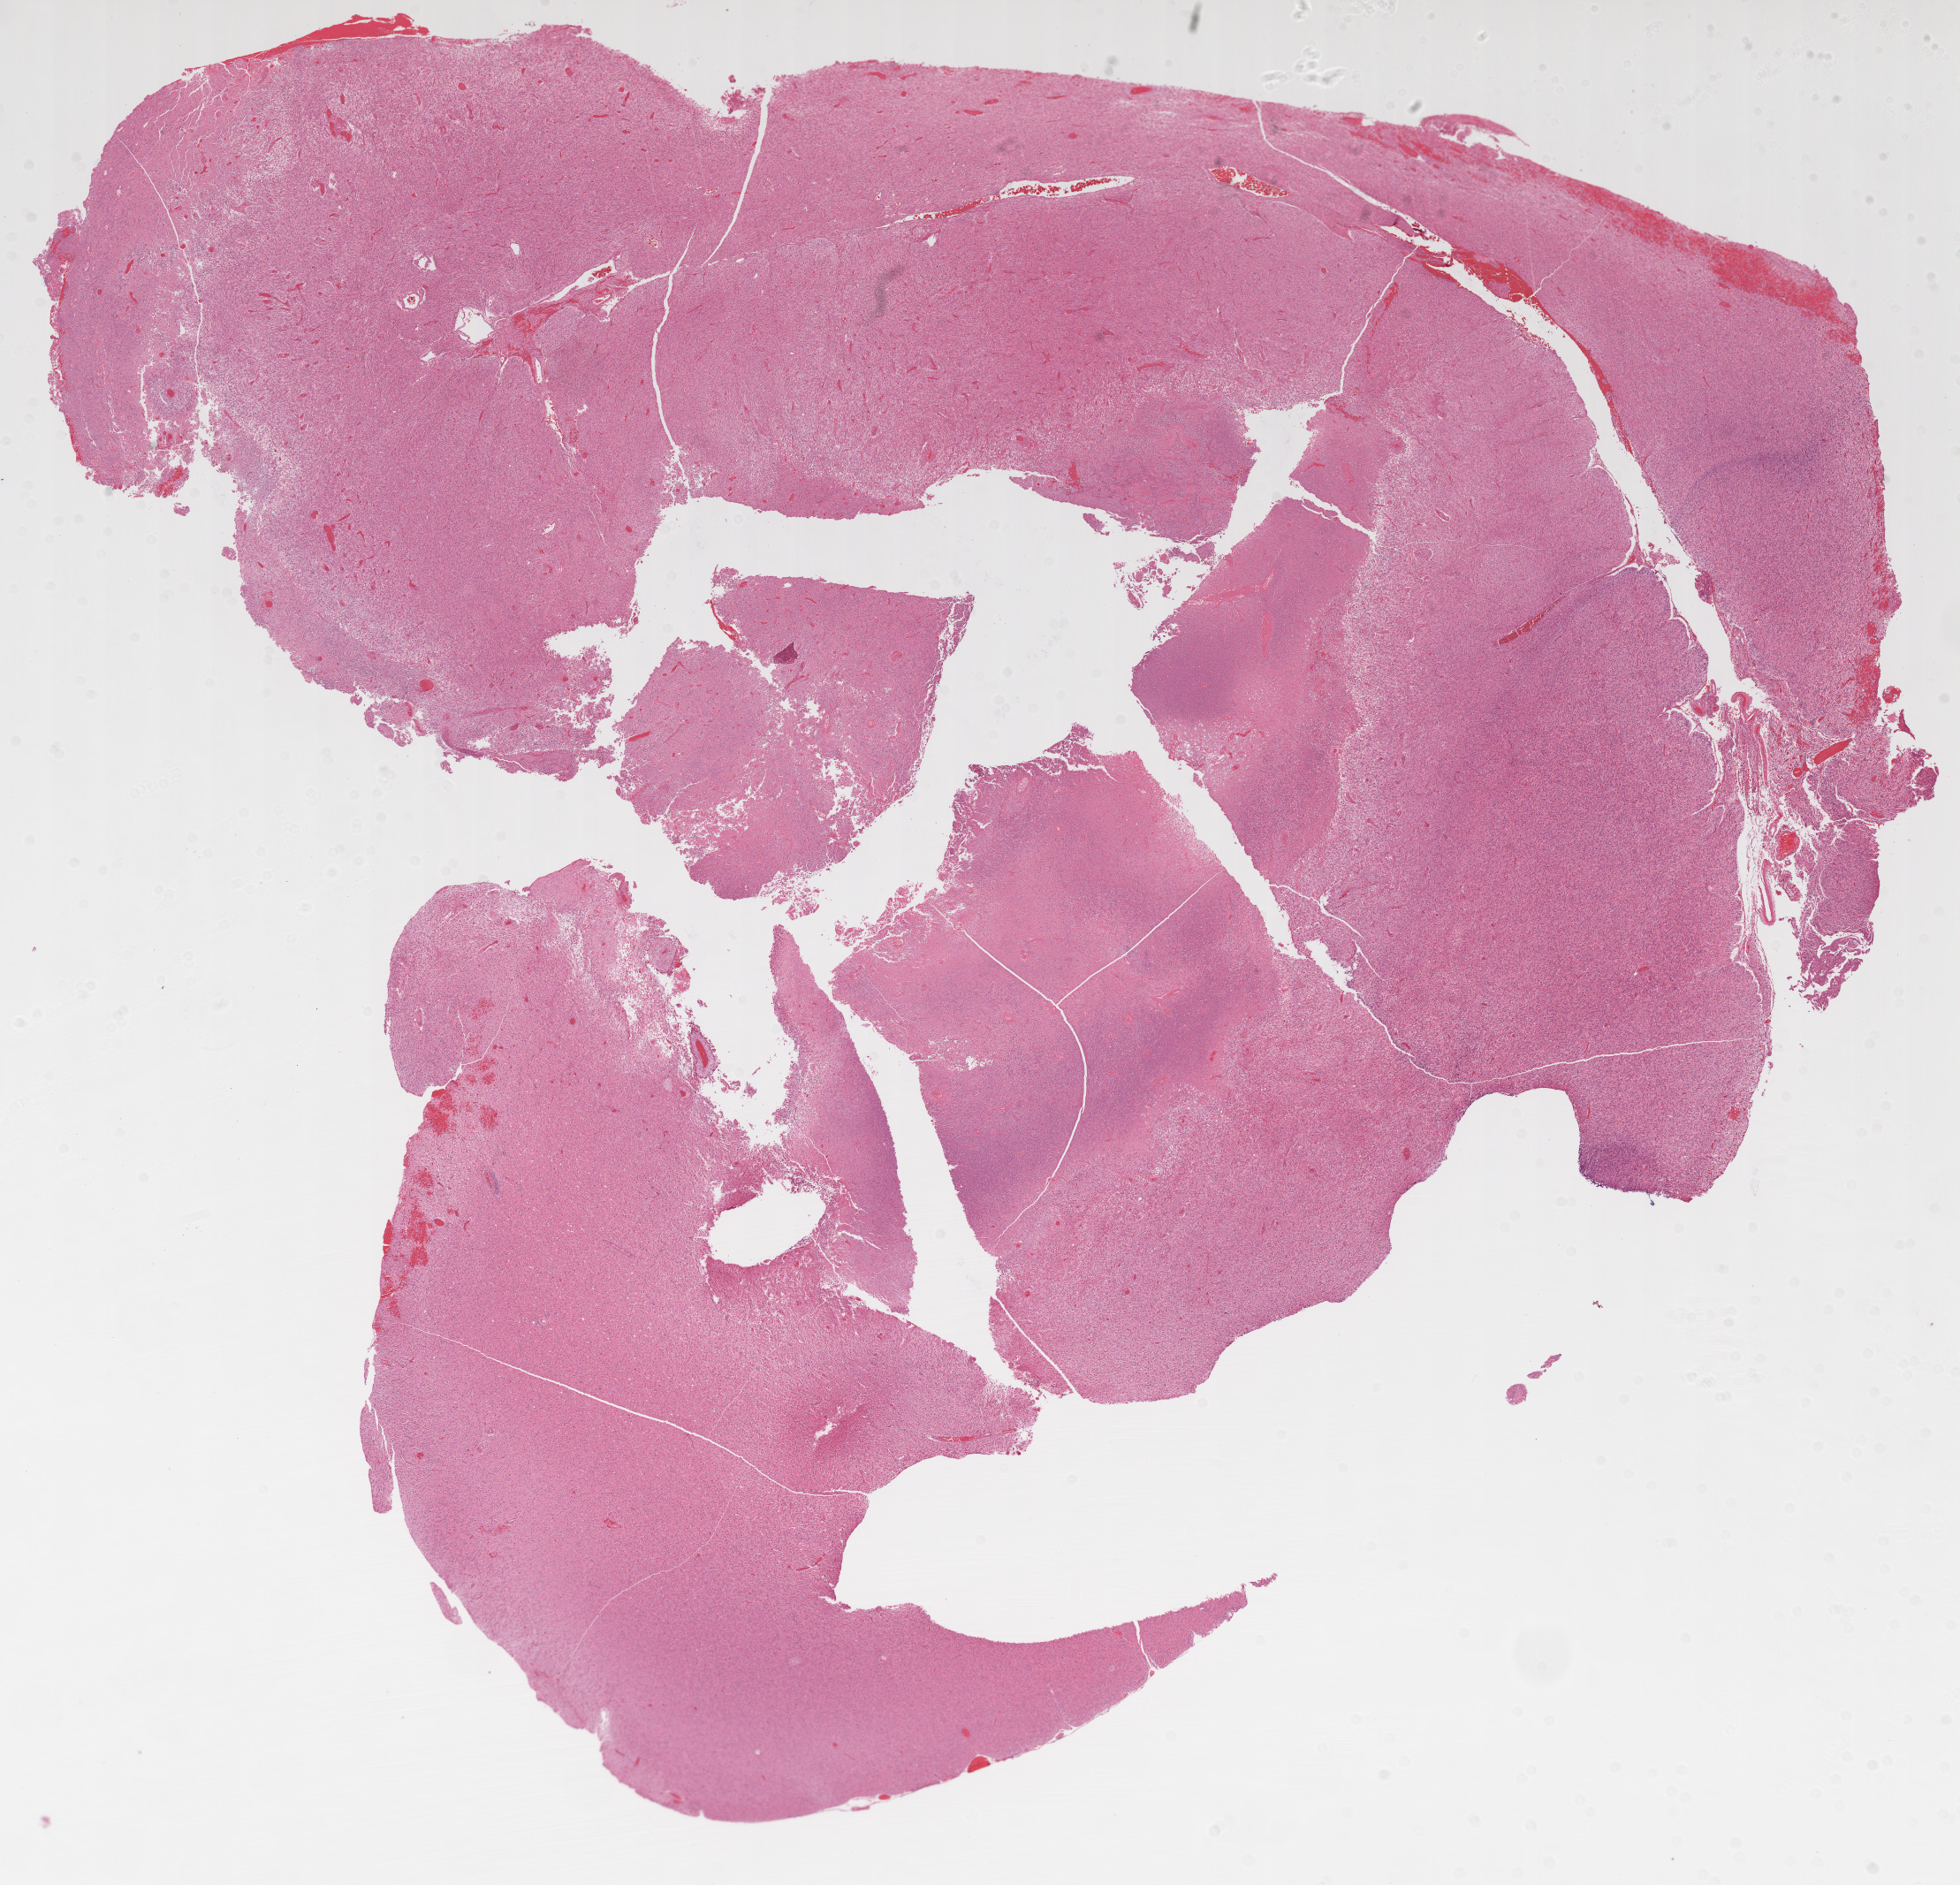
Hematoxylin and eosin (H&E) stained whole-slide image — a low-resolution overview of the entire scanned area, about 17.9 x 17.2 mm; formalin-fixed paraffin-embedded (FFPE) diagnostic section; primary tumour sample from the brain. Patient: male, age at initial diagnosis 68 years.
Pathologic diagnosis: Glioblastoma.